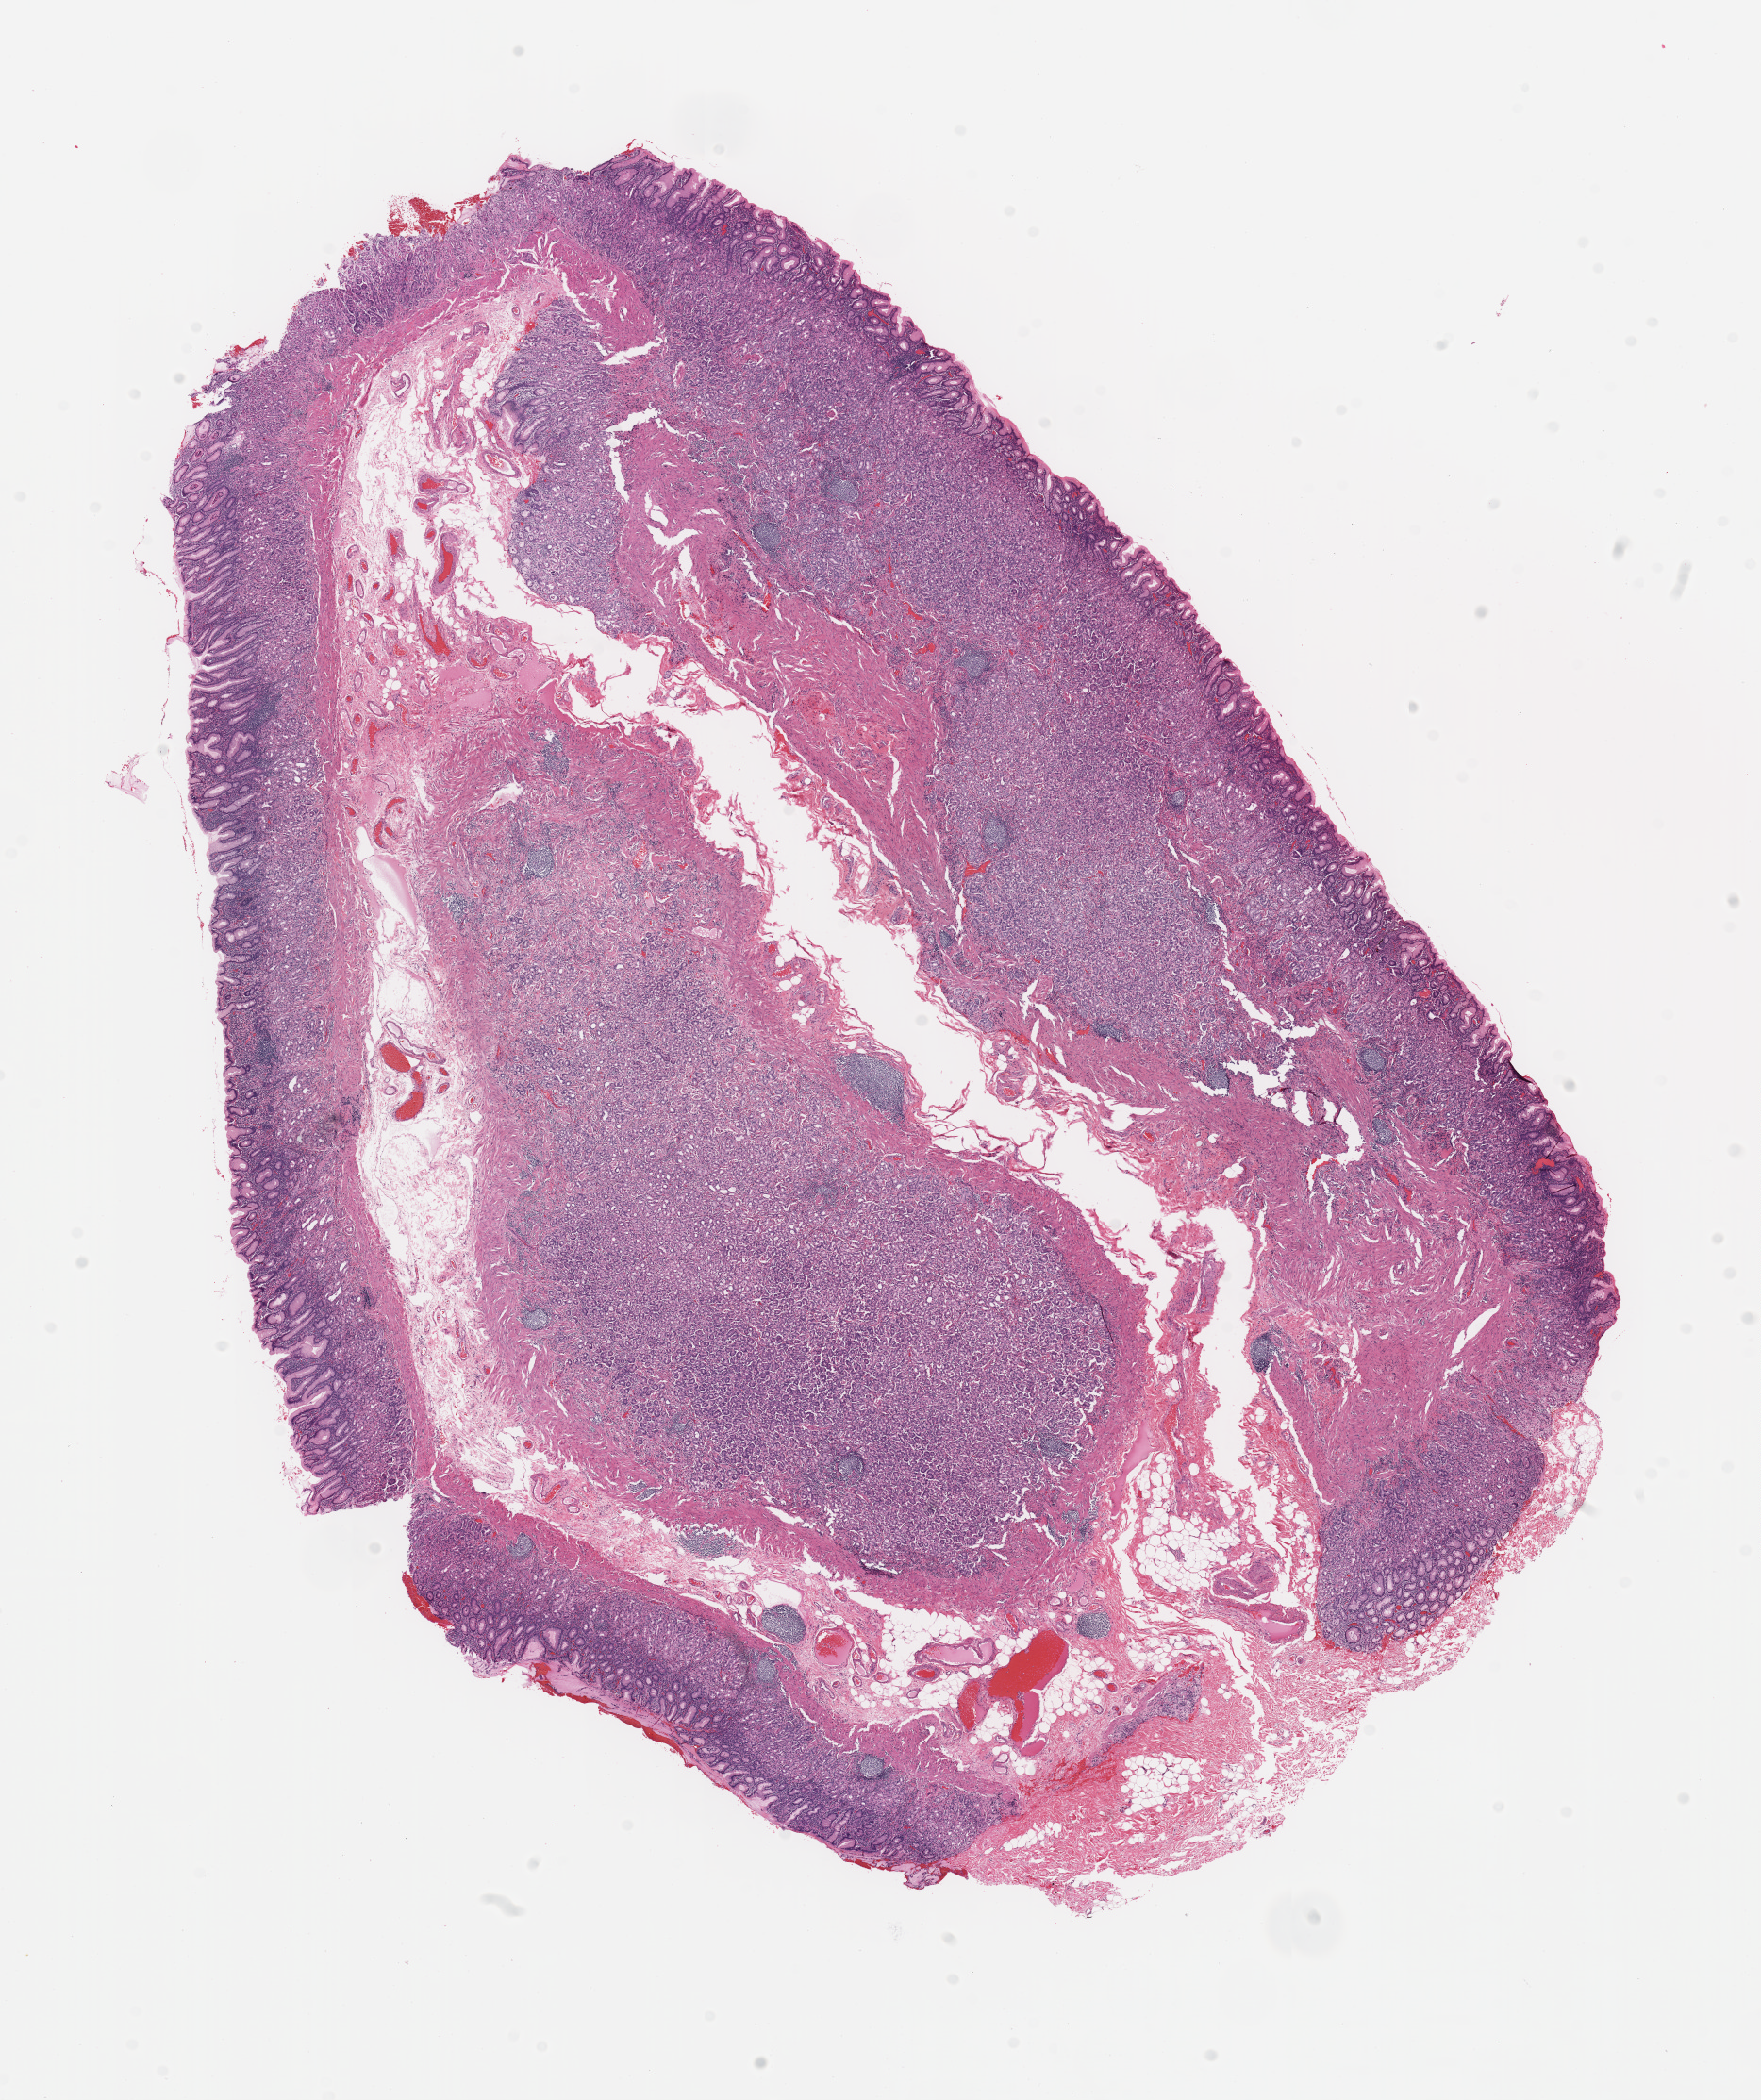
H&E whole-slide image, low-resolution overview of the scanned area, about 14.8 x 17.6 mm (acquisition: 20x scan). 65-year-old female patient.
- patient diagnosis (cohort enrolment): sarcoma (site not recorded at cohort level)